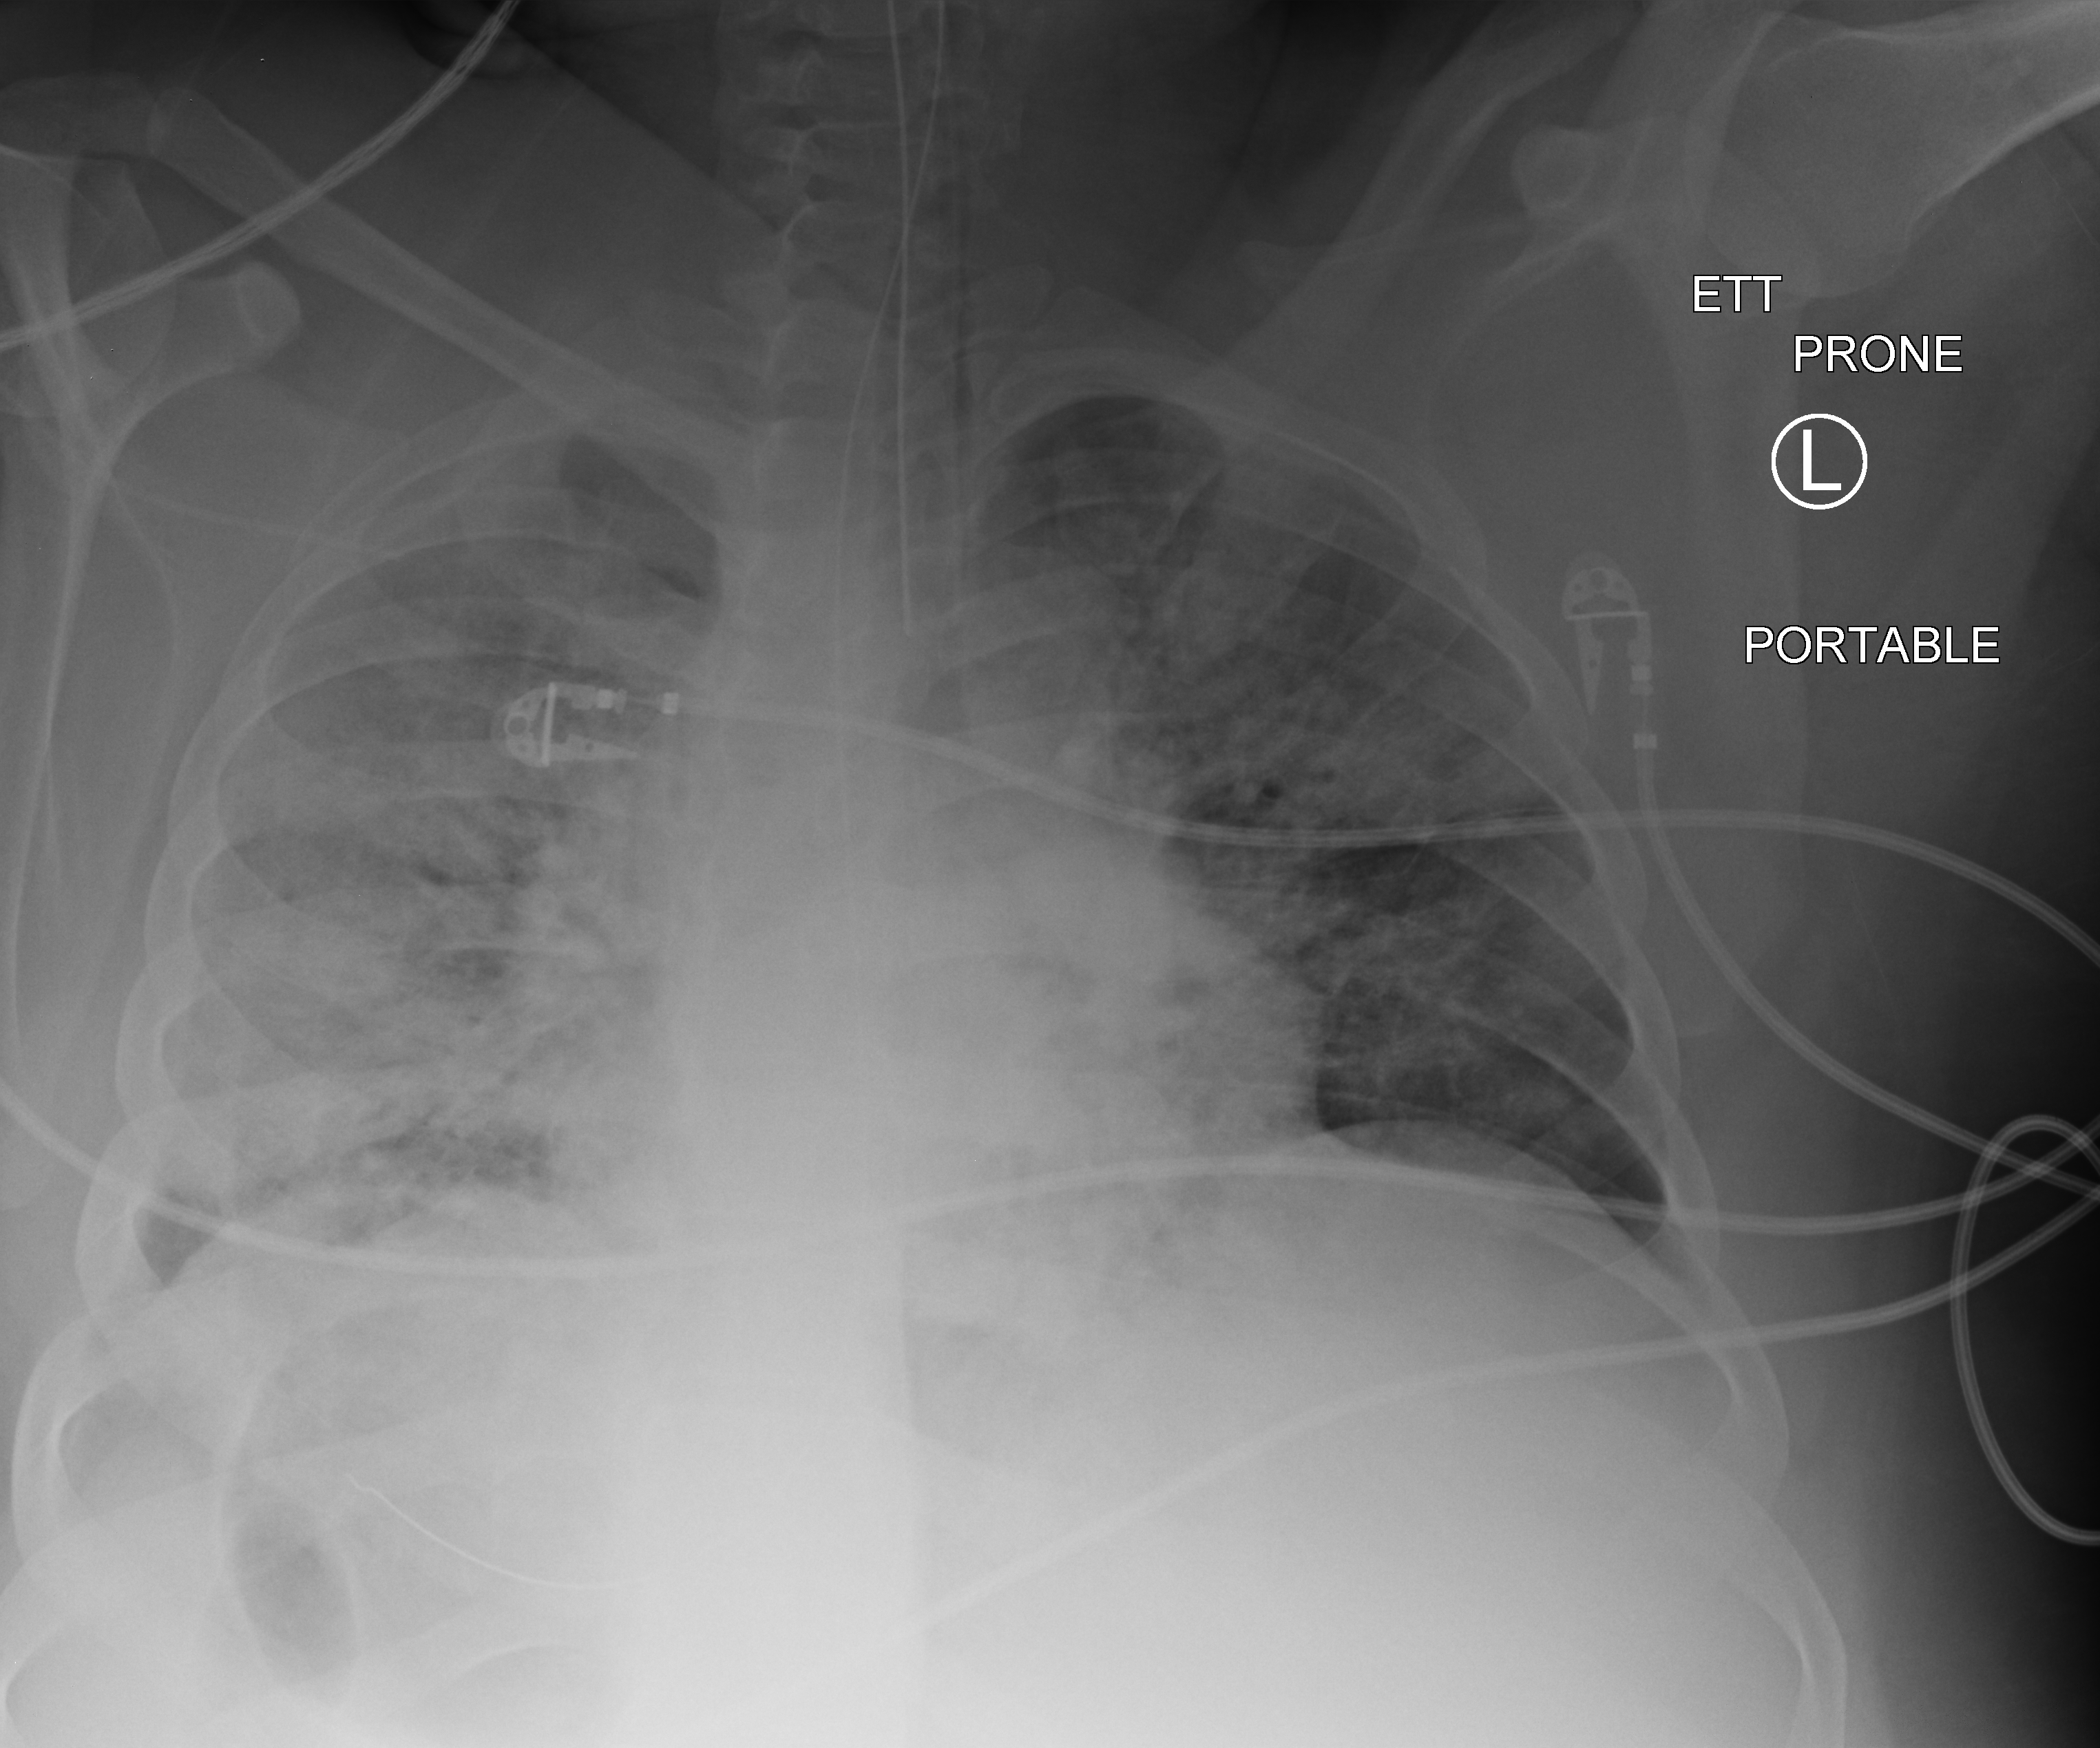
Portable chest radiograph; anteroposterior (AP) projection. Patient hospitalised with COVID-19, aged 18–59 years.
Admission-level facts for this patient (not findings on this image; timing relative to this image not recorded):
- mechanically ventilated during this hospital stay: yes